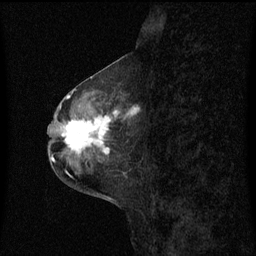
Breast MRI (dynamic contrast-enhanced), one sagittal slice; slice 27 of 60 in the series (ordered by position); dynamic contrast-enhanced series, image 2 of 3 at this slice position (ordered by acquisition); 1.5 T; TE 4.2 ms, TR 8.4 ms; 2 mm slice thickness; 256 × 256 image matrix. Female patient, age 49 years. From the clinical record (not read from this slice): setting: breast cancer imaged before/during neoadjuvant chemotherapy; receptor status: HR-positive, HER2-negative.
Outlined on this slice (semi-automatic segmentation, software-assisted and operator-edited):
- analysis volume of interest (the breast-tissue region the enhancement analysis was run in; not a lesion): box from (x=59, y=101) to (x=136, y=158) px
- tumour enhancement mask (voxels above the 70 % enhancement threshold inside the analysis volume of interest): (x=66, y=110)–(x=136, y=154)